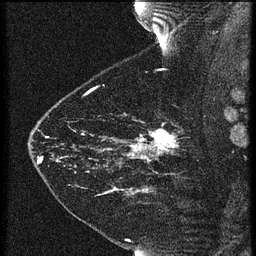
Breast MRI (dynamic contrast-enhanced), one sagittal slice; position 50 of 60 along the scan axis; 3 images stored at this slice position (order not interpretable as contrast timing); 1.5 T; TE 4.2 ms, TR 21.3 ms; 1.5 mm slice thickness; 256 × 256 image matrix, field of view 180 × 180 mm. Female patient, age 43 years. From the clinical record (not read from this slice): setting: breast cancer imaged before/during neoadjuvant chemotherapy; receptor status: HER2-positive.
Outlined on this slice (semi-automatically segmented with operator editing):
- analysis volume of interest (the breast-tissue region the enhancement analysis was run in; not a lesion): bounding box [x1, y1, x2, y2] px = [119, 114, 189, 173]
- tumour enhancement mask (voxels above the 90 % enhancement threshold inside the analysis volume of interest): [128, 128, 177, 161]